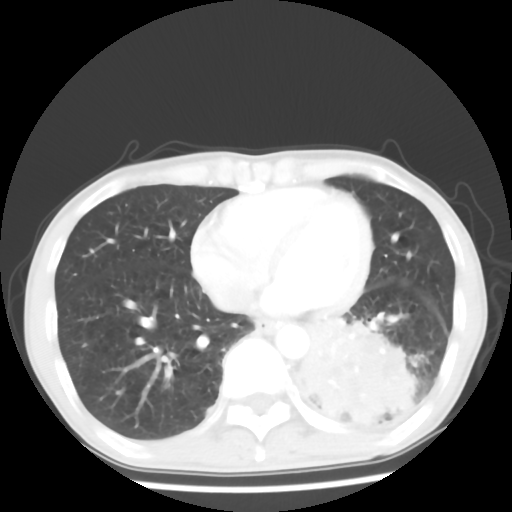
Chest CT, one axial slice; reconstruction kernel STANDARD; 120 kVp; lung window (W 1500 / L -600 HU); 5 mm slice thickness; 512 × 512 image matrix, field of view 313 × 313 mm. Male patient, age 68 years. Case-level facts recorded for this patient, not image findings: clinical TNM (as recorded): T4 N0 M0.
Structures marked on this image (bounding box drawn by a radiologist):
- lung tumour (recorded histology: squamous cell carcinoma): bounding box <293,310,434,442> (left, top, right, bottom; pixels)